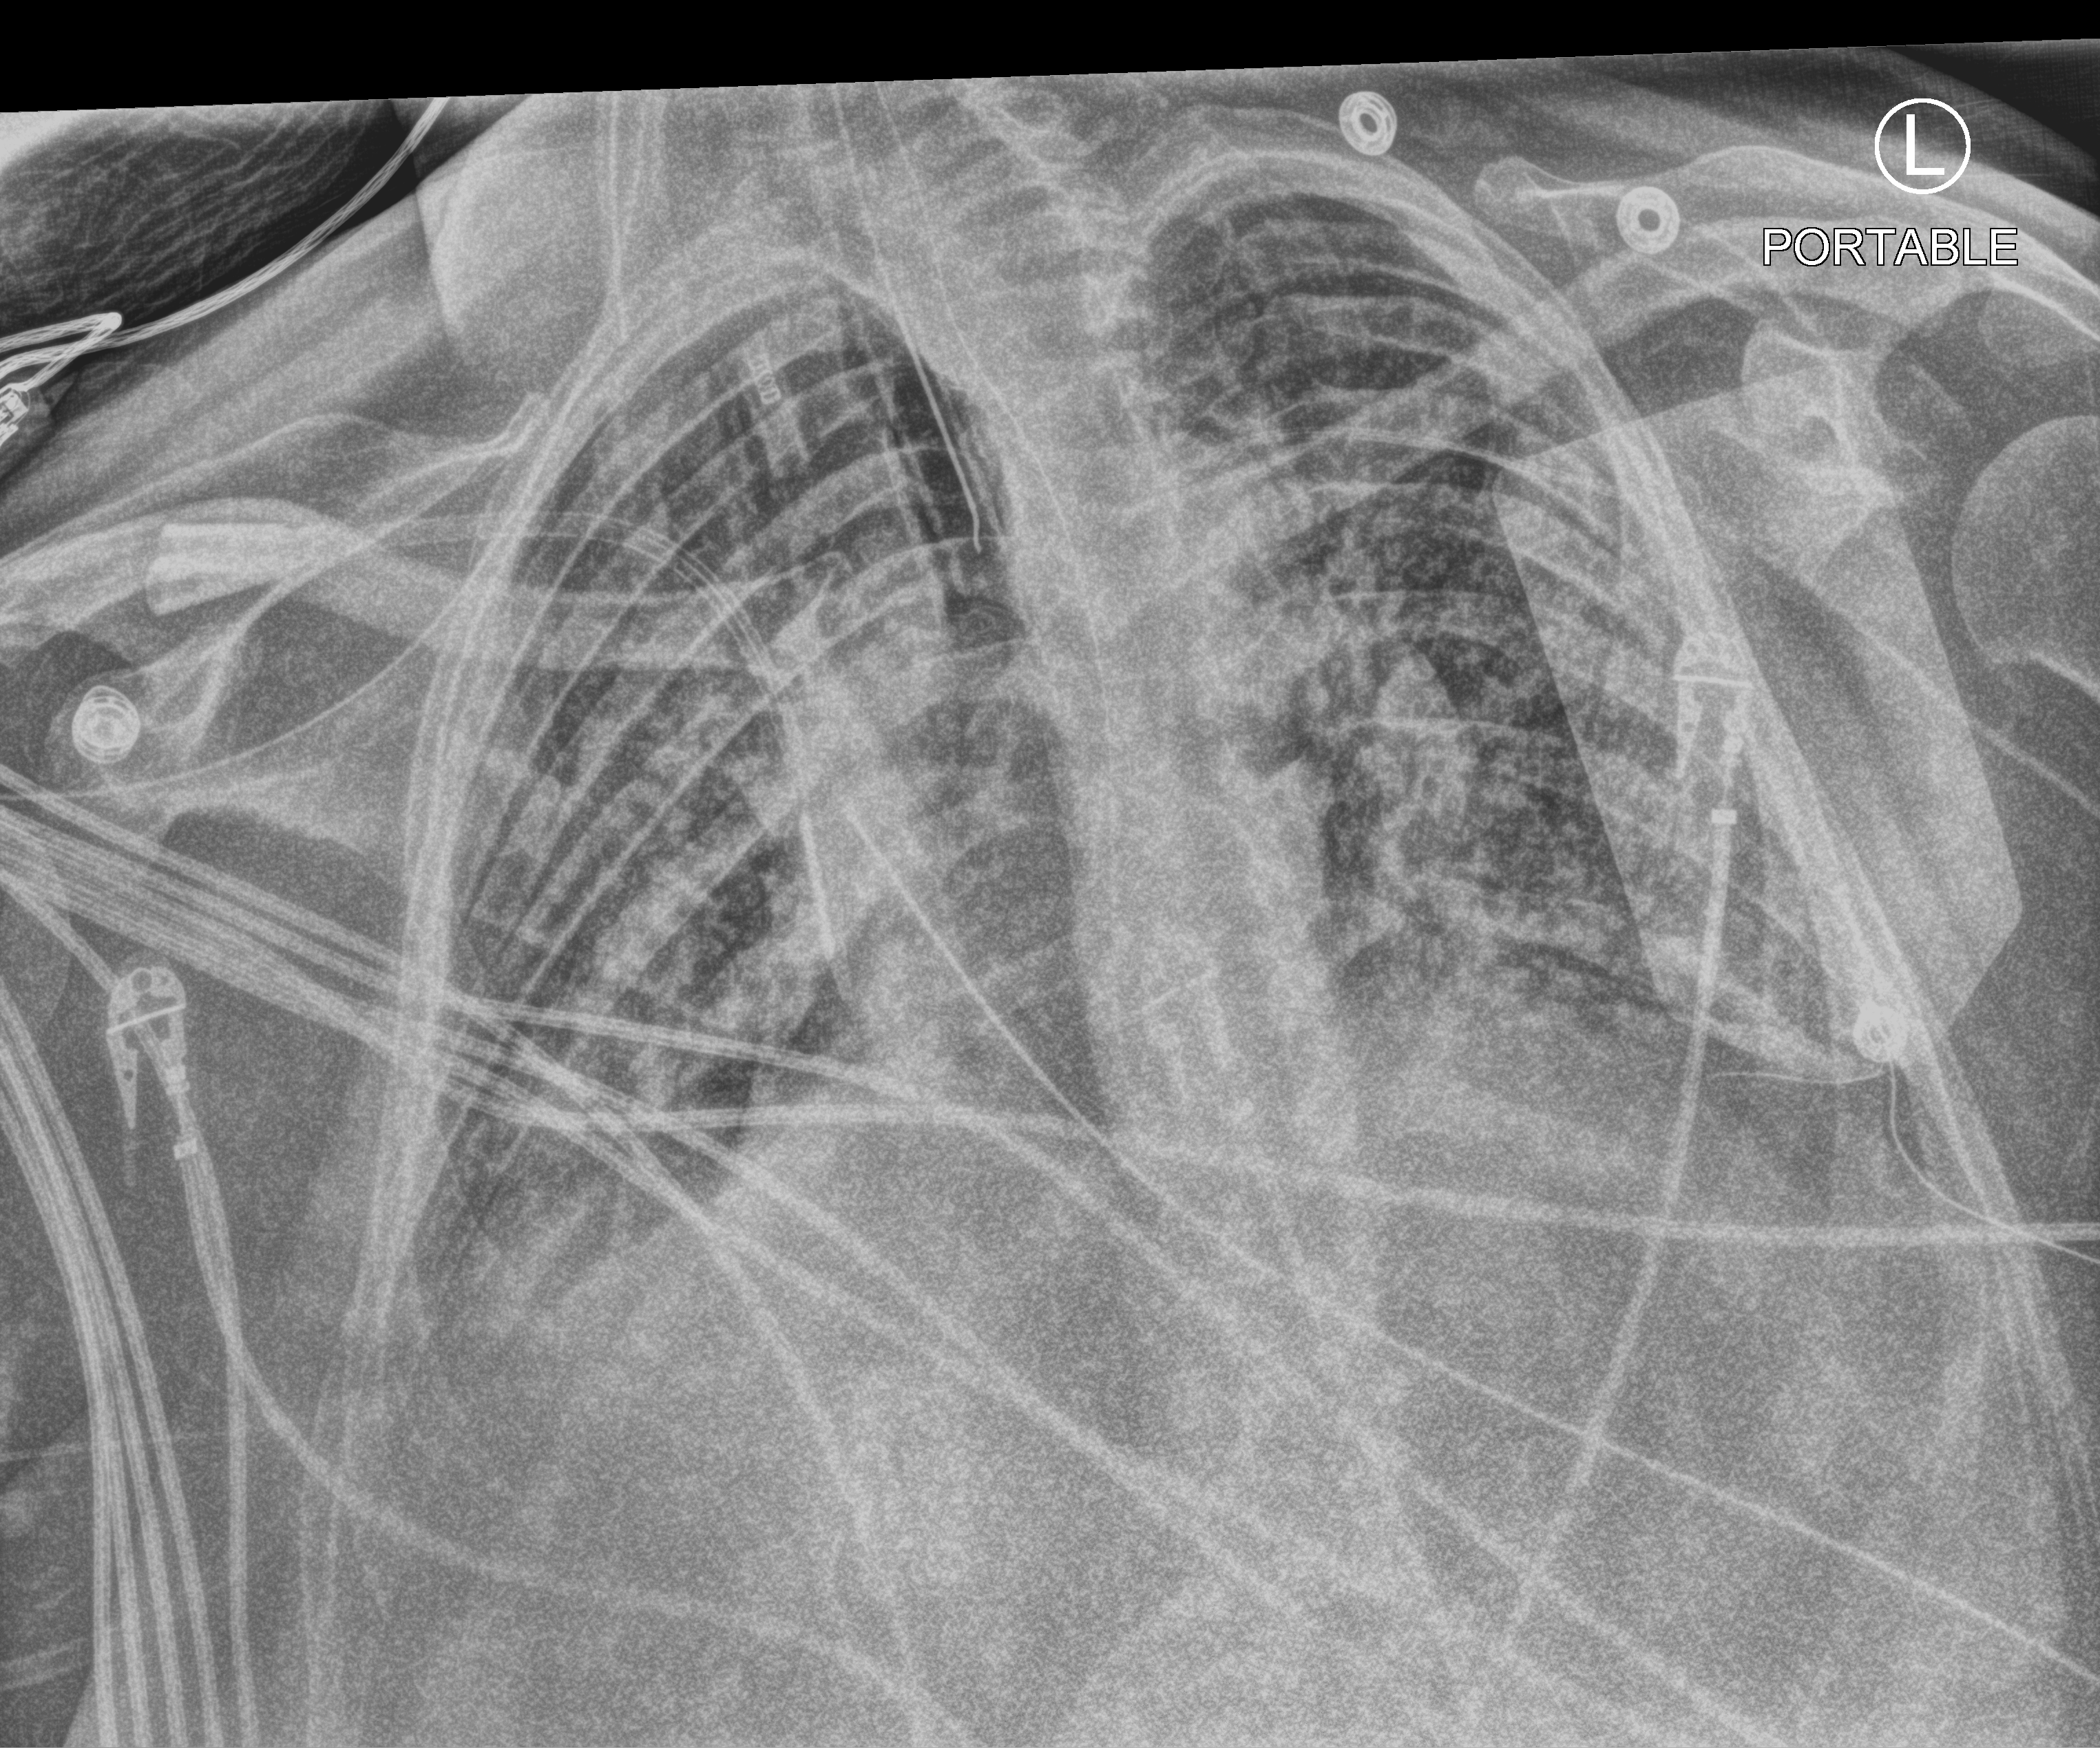
Chest X-ray (portable). Male patient hospitalised with COVID-19, age 18–59 years.
Admission-level facts for this patient (not findings on this image; timing relative to this image not recorded):
- length of hospital stay: 39 days
- mechanically ventilated during this hospital stay: yes